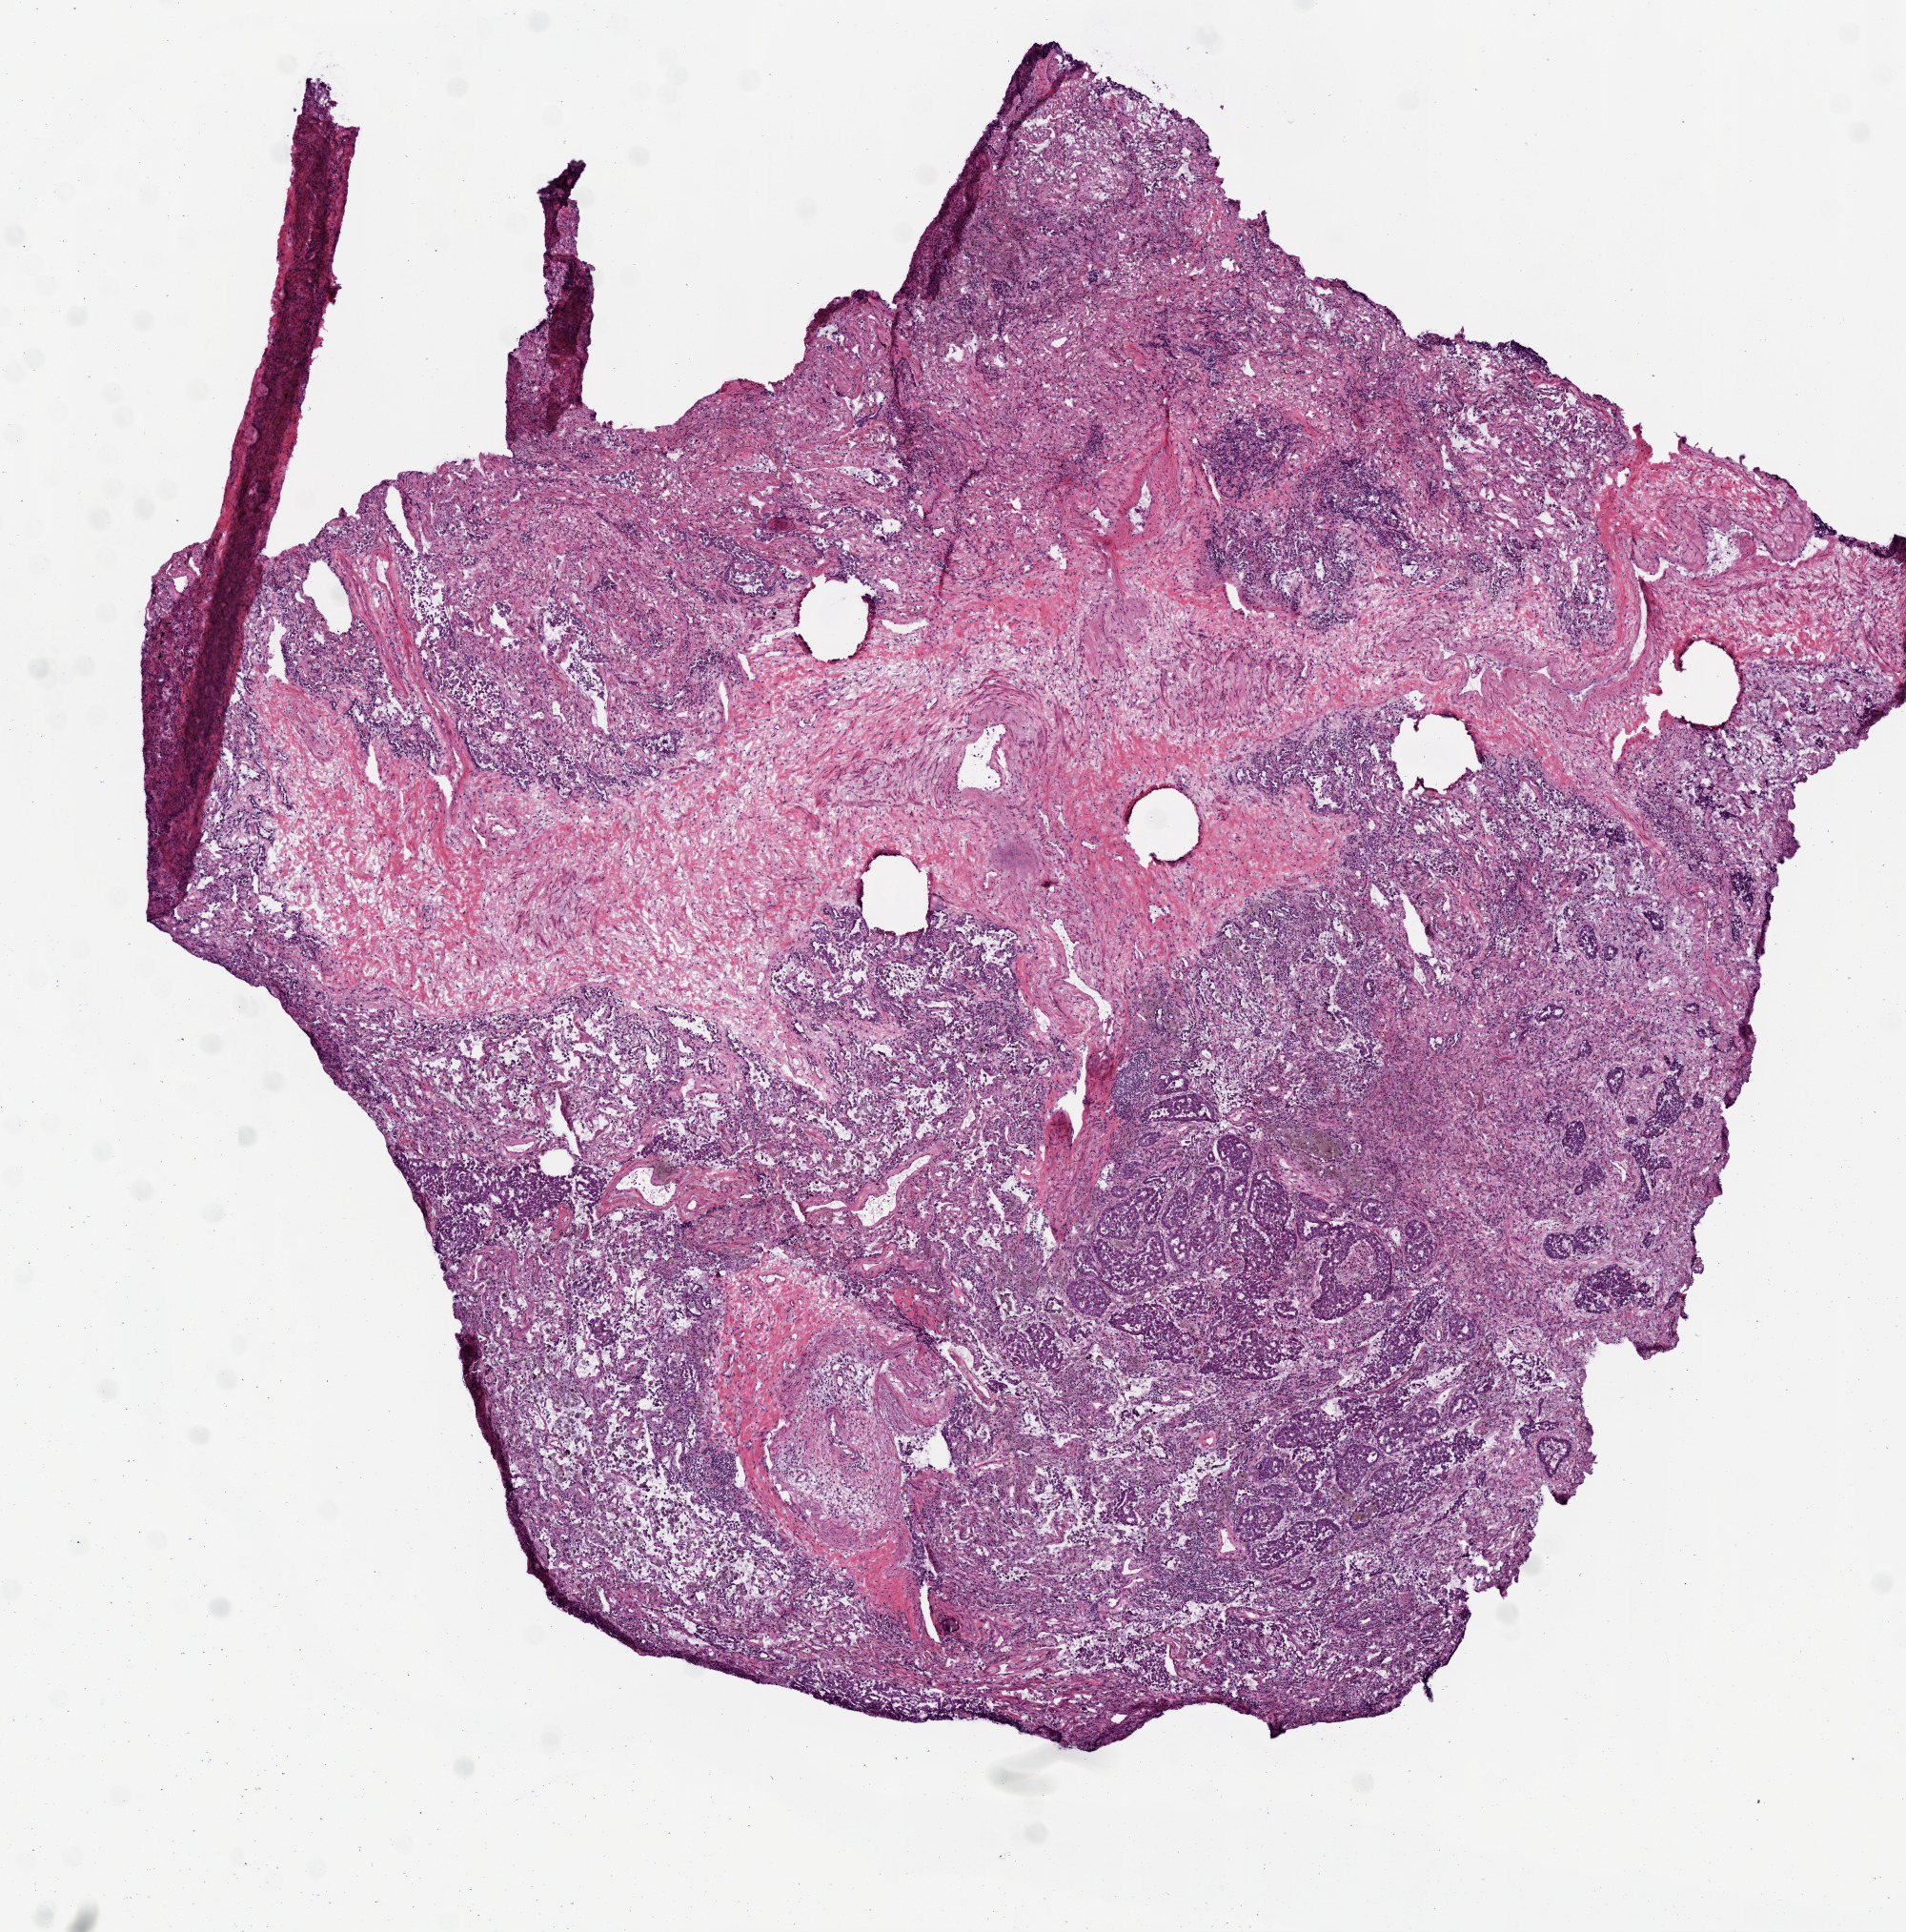
H&E-stained whole-slide image, shown as a low-resolution overview of the whole scanned area (about 8.0 x 8.1 mm, from a 20x scan). Frozen section from the top of the tissue portion. Sample: primary tumour, lung. Male, age 61 years at initial diagnosis. Composition of this section per pathologist review: tumour cells 80%, tumour nuclei 60%, normal cells 5%, stromal cells 15%, necrosis 5%.
AJCC pathologic stage: IA (7th edition). Pathologic diagnosis: Adenocarcinoma, NOS (upper lobe, lung).